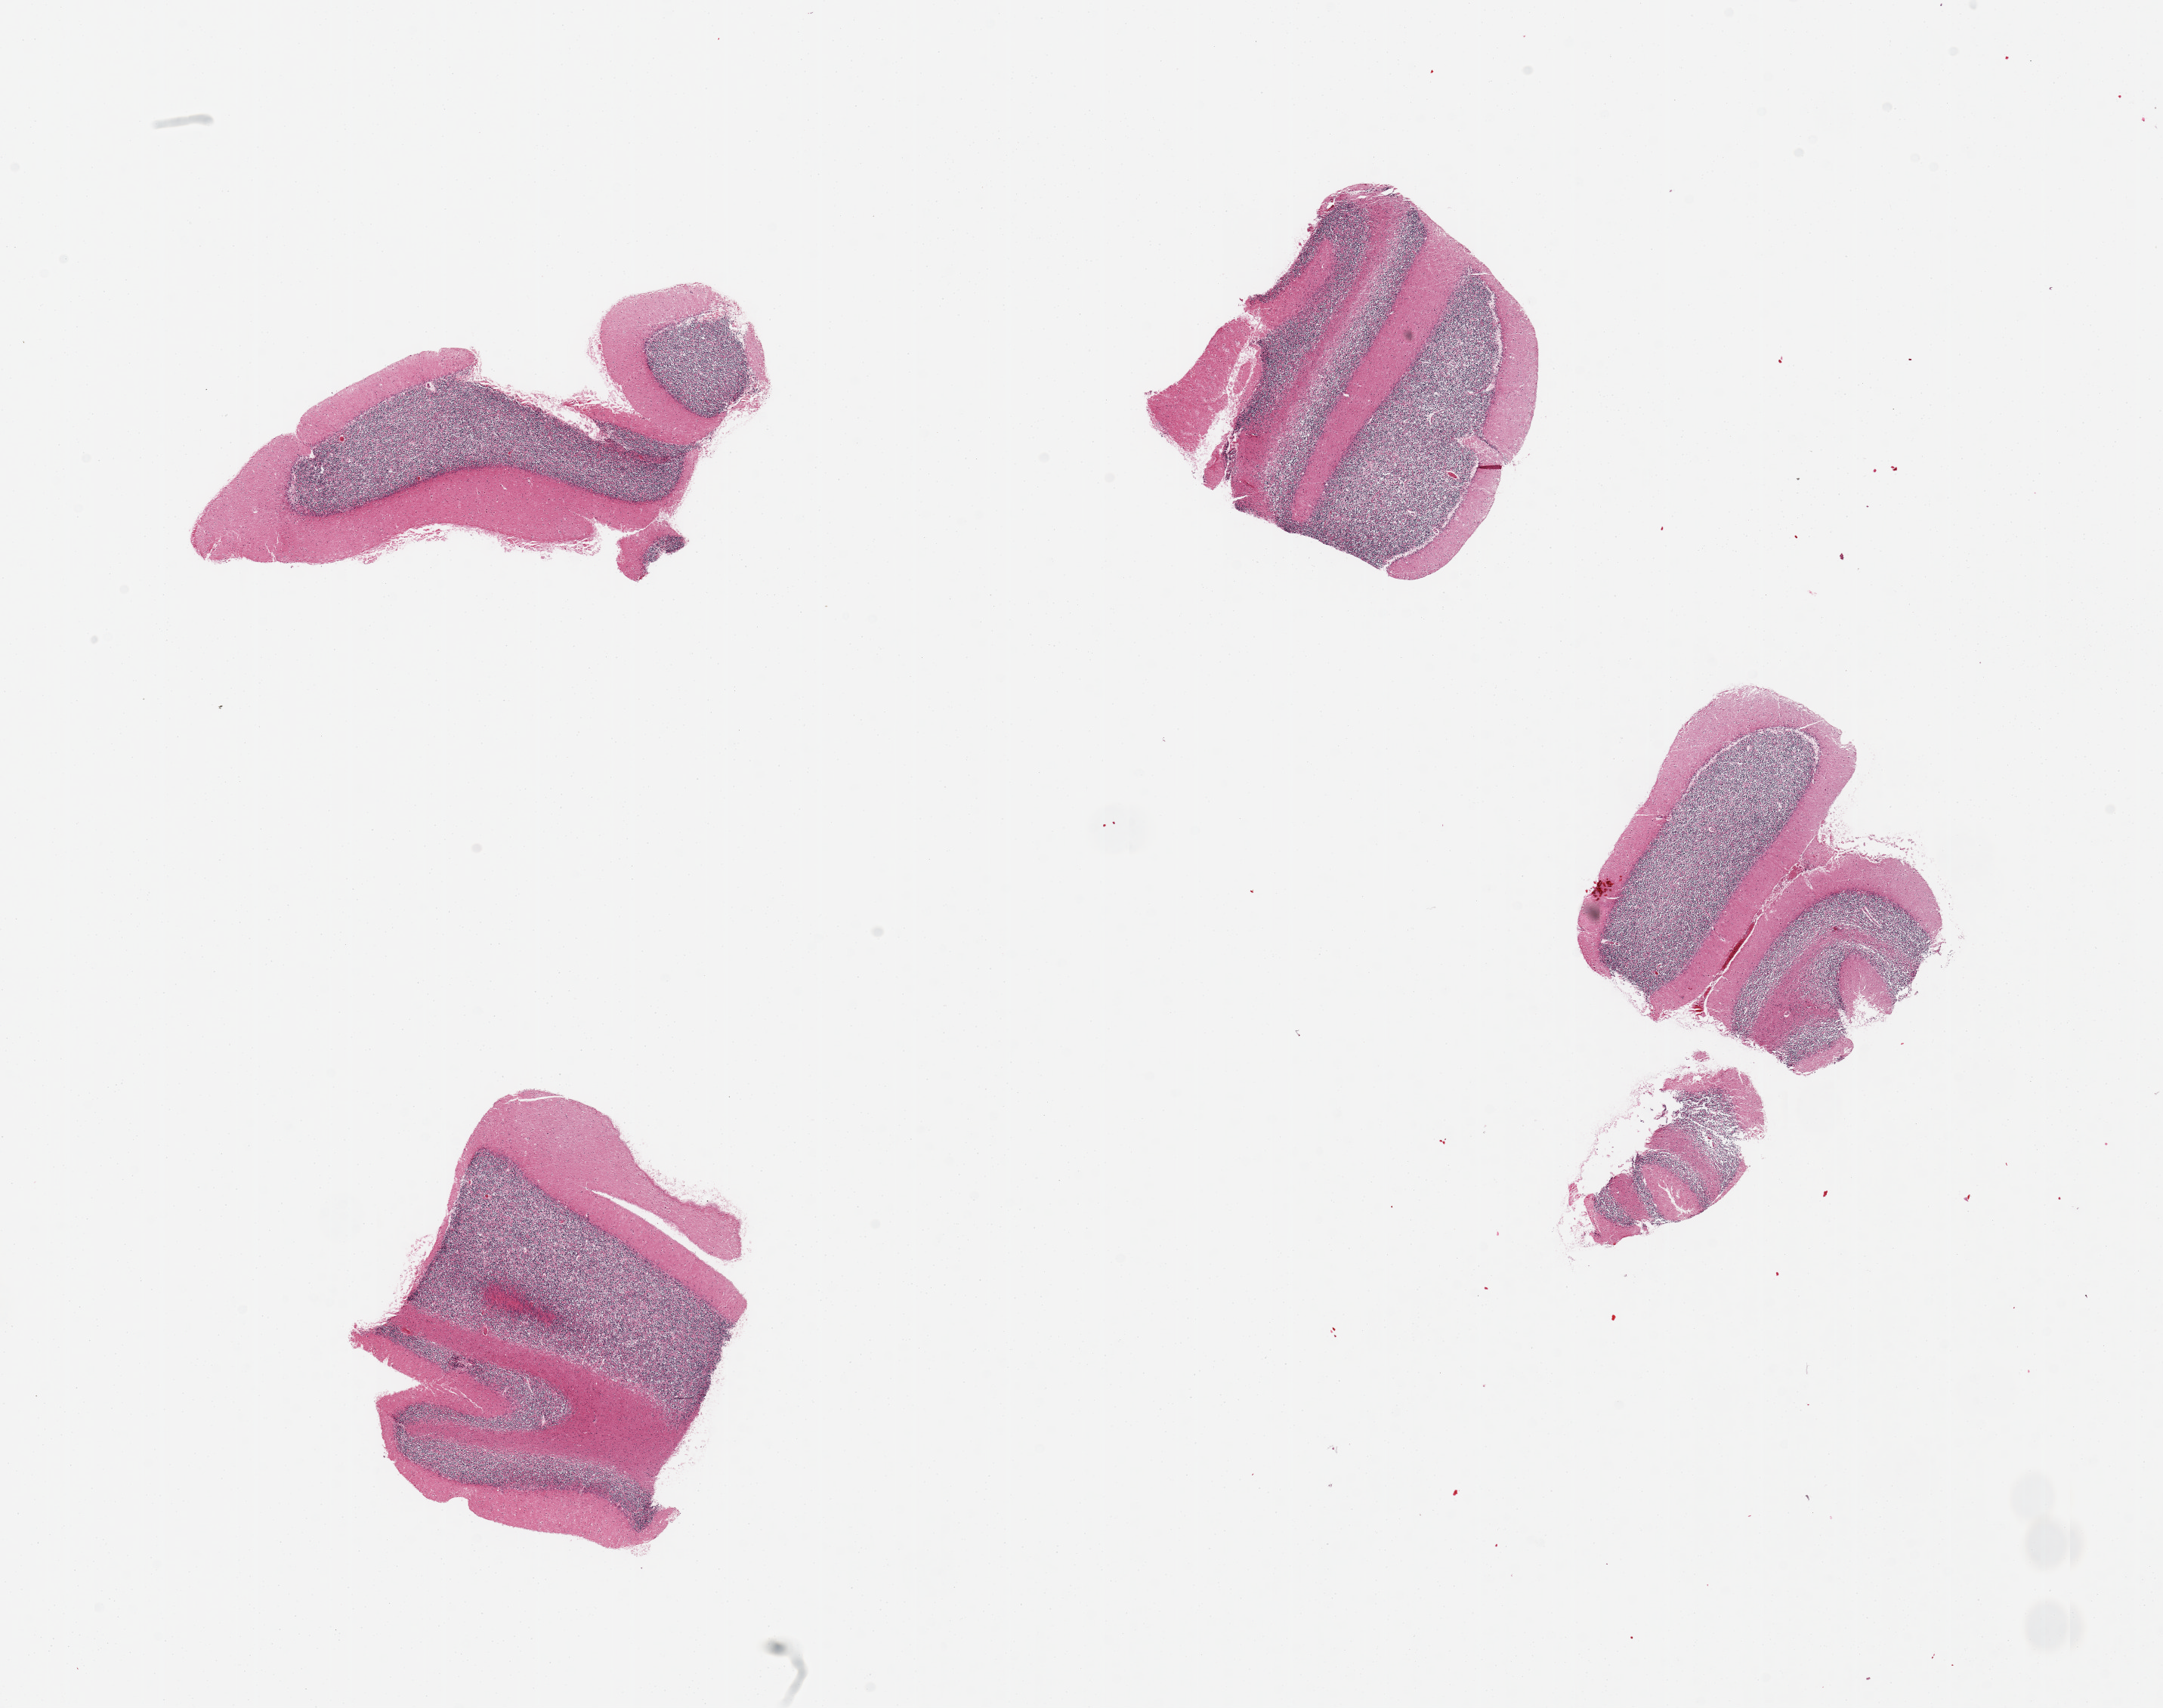
H&E whole-slide image — low-resolution overview of the scanned area, about 22.6 x 17.9 mm (slide scanned at 20x), PAXgene-fixed paraffin-embedded (PFPE) section, target tissue: cerebellum, donor tissue sample. Donor sex: male.
Review note (as recorded): 4 pieces, one fragmented, moderate autolysis.